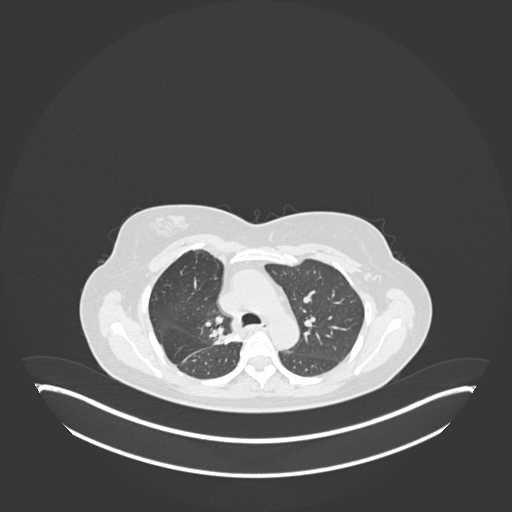
Chest CT, one axial slice. Position 118 of 181 along the scan axis. 120 kVp. Lung window (W 1500 / L -600 HU). 1 mm slice thickness. 512 × 512 image matrix, field of view 500 × 500 mm. Female patient, age 65 years. Case-level facts recorded for this patient, not image findings: clinical TNM (as recorded): T1b N0 M0; histopathological grade: G2.
Annotated regions visible in this slice (rectangle marked by the reading radiologist):
- lung tumour (recorded histology: adenocarcinoma): bounding box (x1, y1, x2, y2) in pixels: (209, 326, 244, 349)